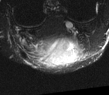
MRI of an extremity soft-tissue mass, one axial slice; position 14 of 52 along the scan axis; T2-weighted fat-saturated; MR volume resampled by the dataset authors to the PET/CT grid (not the native acquisition matrix); 3.27 mm slice thickness; 109 × 95 image matrix, field of view 106 × 93 mm. Male patient. From the clinical record (not read from this slice): histological type: synovial sarcoma; site of the primary tumour: left poplietal fossa.
Annotated regions visible in this slice (expert contour drawn on MRI and transferred to this co-registered scan by the dataset authors):
- gross tumour volume (mass): bounding box <37,35,80,66> (left, top, right, bottom; pixels)